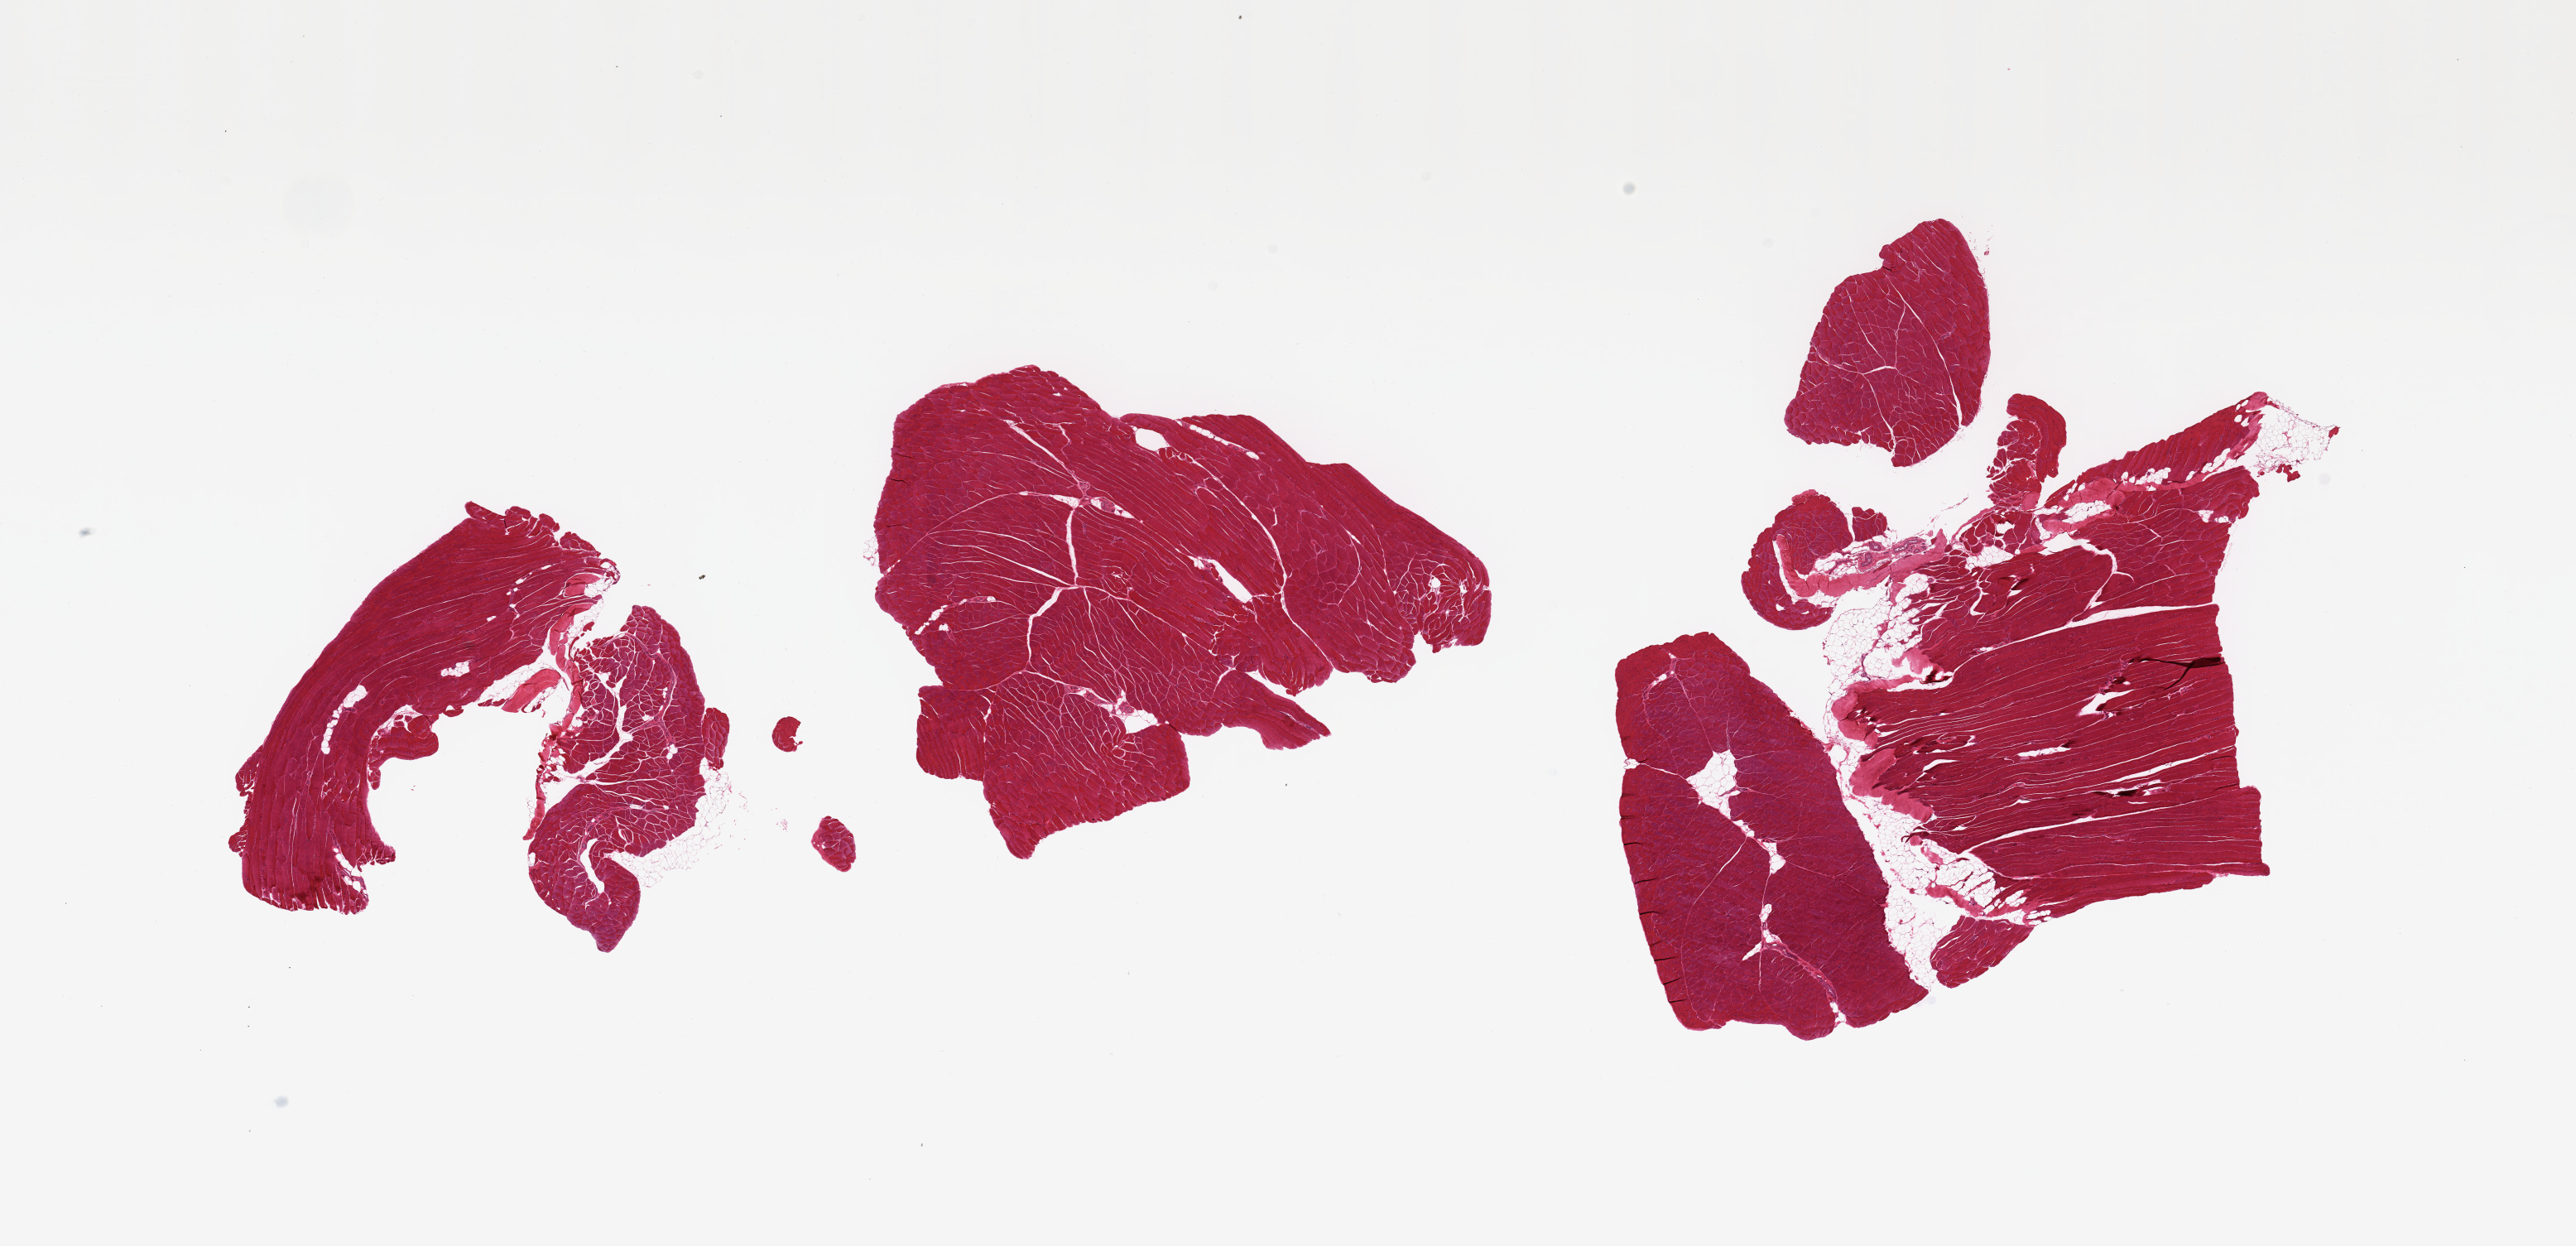
Haematoxylin and eosin whole-slide image, brightfield, whole scanned area (about 24.6 x 11.9 mm, slide scanned at 20x) shown as a low-resolution overview, PAXgene-fixed, paraffin-embedded tissue, section of skeletal muscle (target tissue), tissue donor sample. Donor: female.
- pathologist's review note for this sample: 3 pieces; focal (5%) admixture with dense collagen (tendon) on 2 pieces